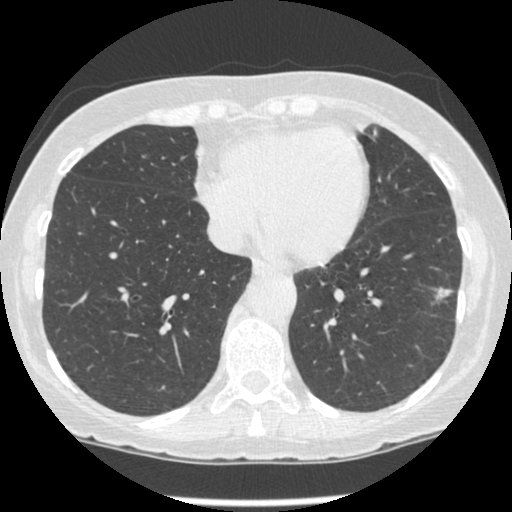
Low-dose screening chest CT, one axial slice; lung window (W 1500 / L -600 HU); 1.25 mm slice thickness; 512 × 512 image matrix, field of view 303 × 303 mm.
Structures marked on this image (outlined manually by an expert reader):
- lesion 1 (tumor, lower lobe of left lung): box from (x=435, y=288) to (x=452, y=300) px